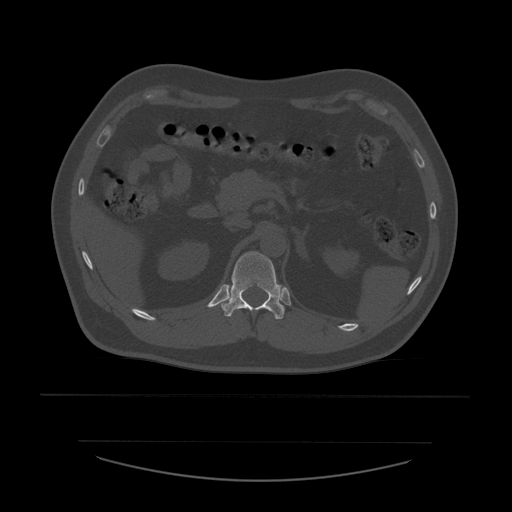
CT including the spine, one axial slice; slice 252 of 532 in the series (ordered by position); 120 kVp; bone window (W 1800 / L 400 HU); 1.25 mm slice thickness; 512 × 512 image matrix, field of view 441 × 441 mm. Patient age 44 years. Case-level facts recorded for this patient, not image findings: primary cancer: soft tissue sarcoma.
Structures marked on this image (semi-automatically segmented with operator editing):
- T12 vertebra: box from (x=221, y=252) to (x=285, y=320) px